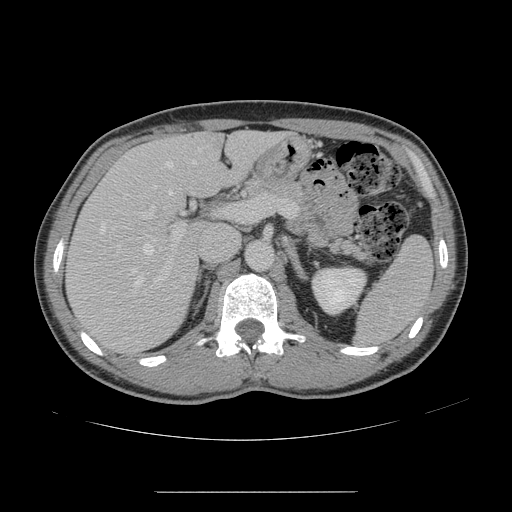
Contrast-enhanced abdominal CT, one axial slice. Slice 88 of 178 in the series (ordered by position). 120 kVp. Intravenous contrast given. Soft-tissue window (W 400 / L 40 HU). 2.5 mm slice thickness. 512 × 512 image matrix, field of view 401 × 401 mm. Male patient, age 53 years. Case-level facts recorded for this patient, not image findings: diagnosis: colorectal cancer liver metastases, imaged before liver resection; multiple liver metastases: yes; largest metastasis: 2.4 cm; chemotherapy before resection: yes.
Structures marked on this image (manually delineated by an expert):
- hepatic veins: box from (x=99, y=148) to (x=201, y=290) px
- liver: (x=68, y=132)–(x=281, y=352)
- planned liver remnant (the part of the liver to remain after resection): (x=151, y=132)–(x=280, y=195)
- portal vein (with intrahepatic branches): (x=139, y=194)–(x=267, y=288)